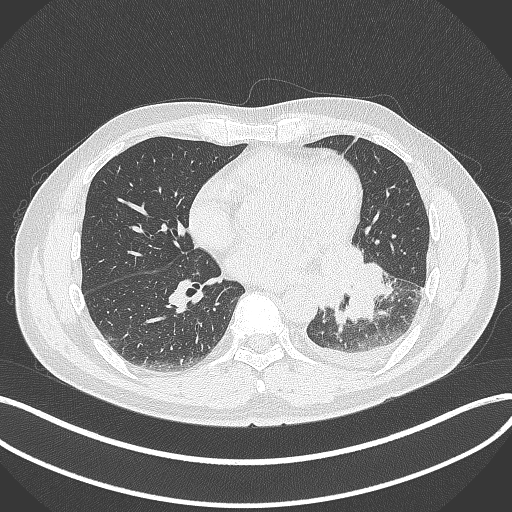
Chest CT, one axial slice; reconstruction kernel B70f; lung window (W 1500 / L -600 HU); 1 mm slice thickness; 512 × 512 image matrix. Male patient, age 58 years. Case-level facts recorded for this patient, not image findings: clinical TNM (as recorded): T3 N1 M1b; histopathological grade: G3.
Annotated regions visible in this slice (rectangle marked by the reading radiologist):
- lung tumour (recorded histology: small cell carcinoma): bounding box <323,238,385,332> (left, top, right, bottom; pixels)